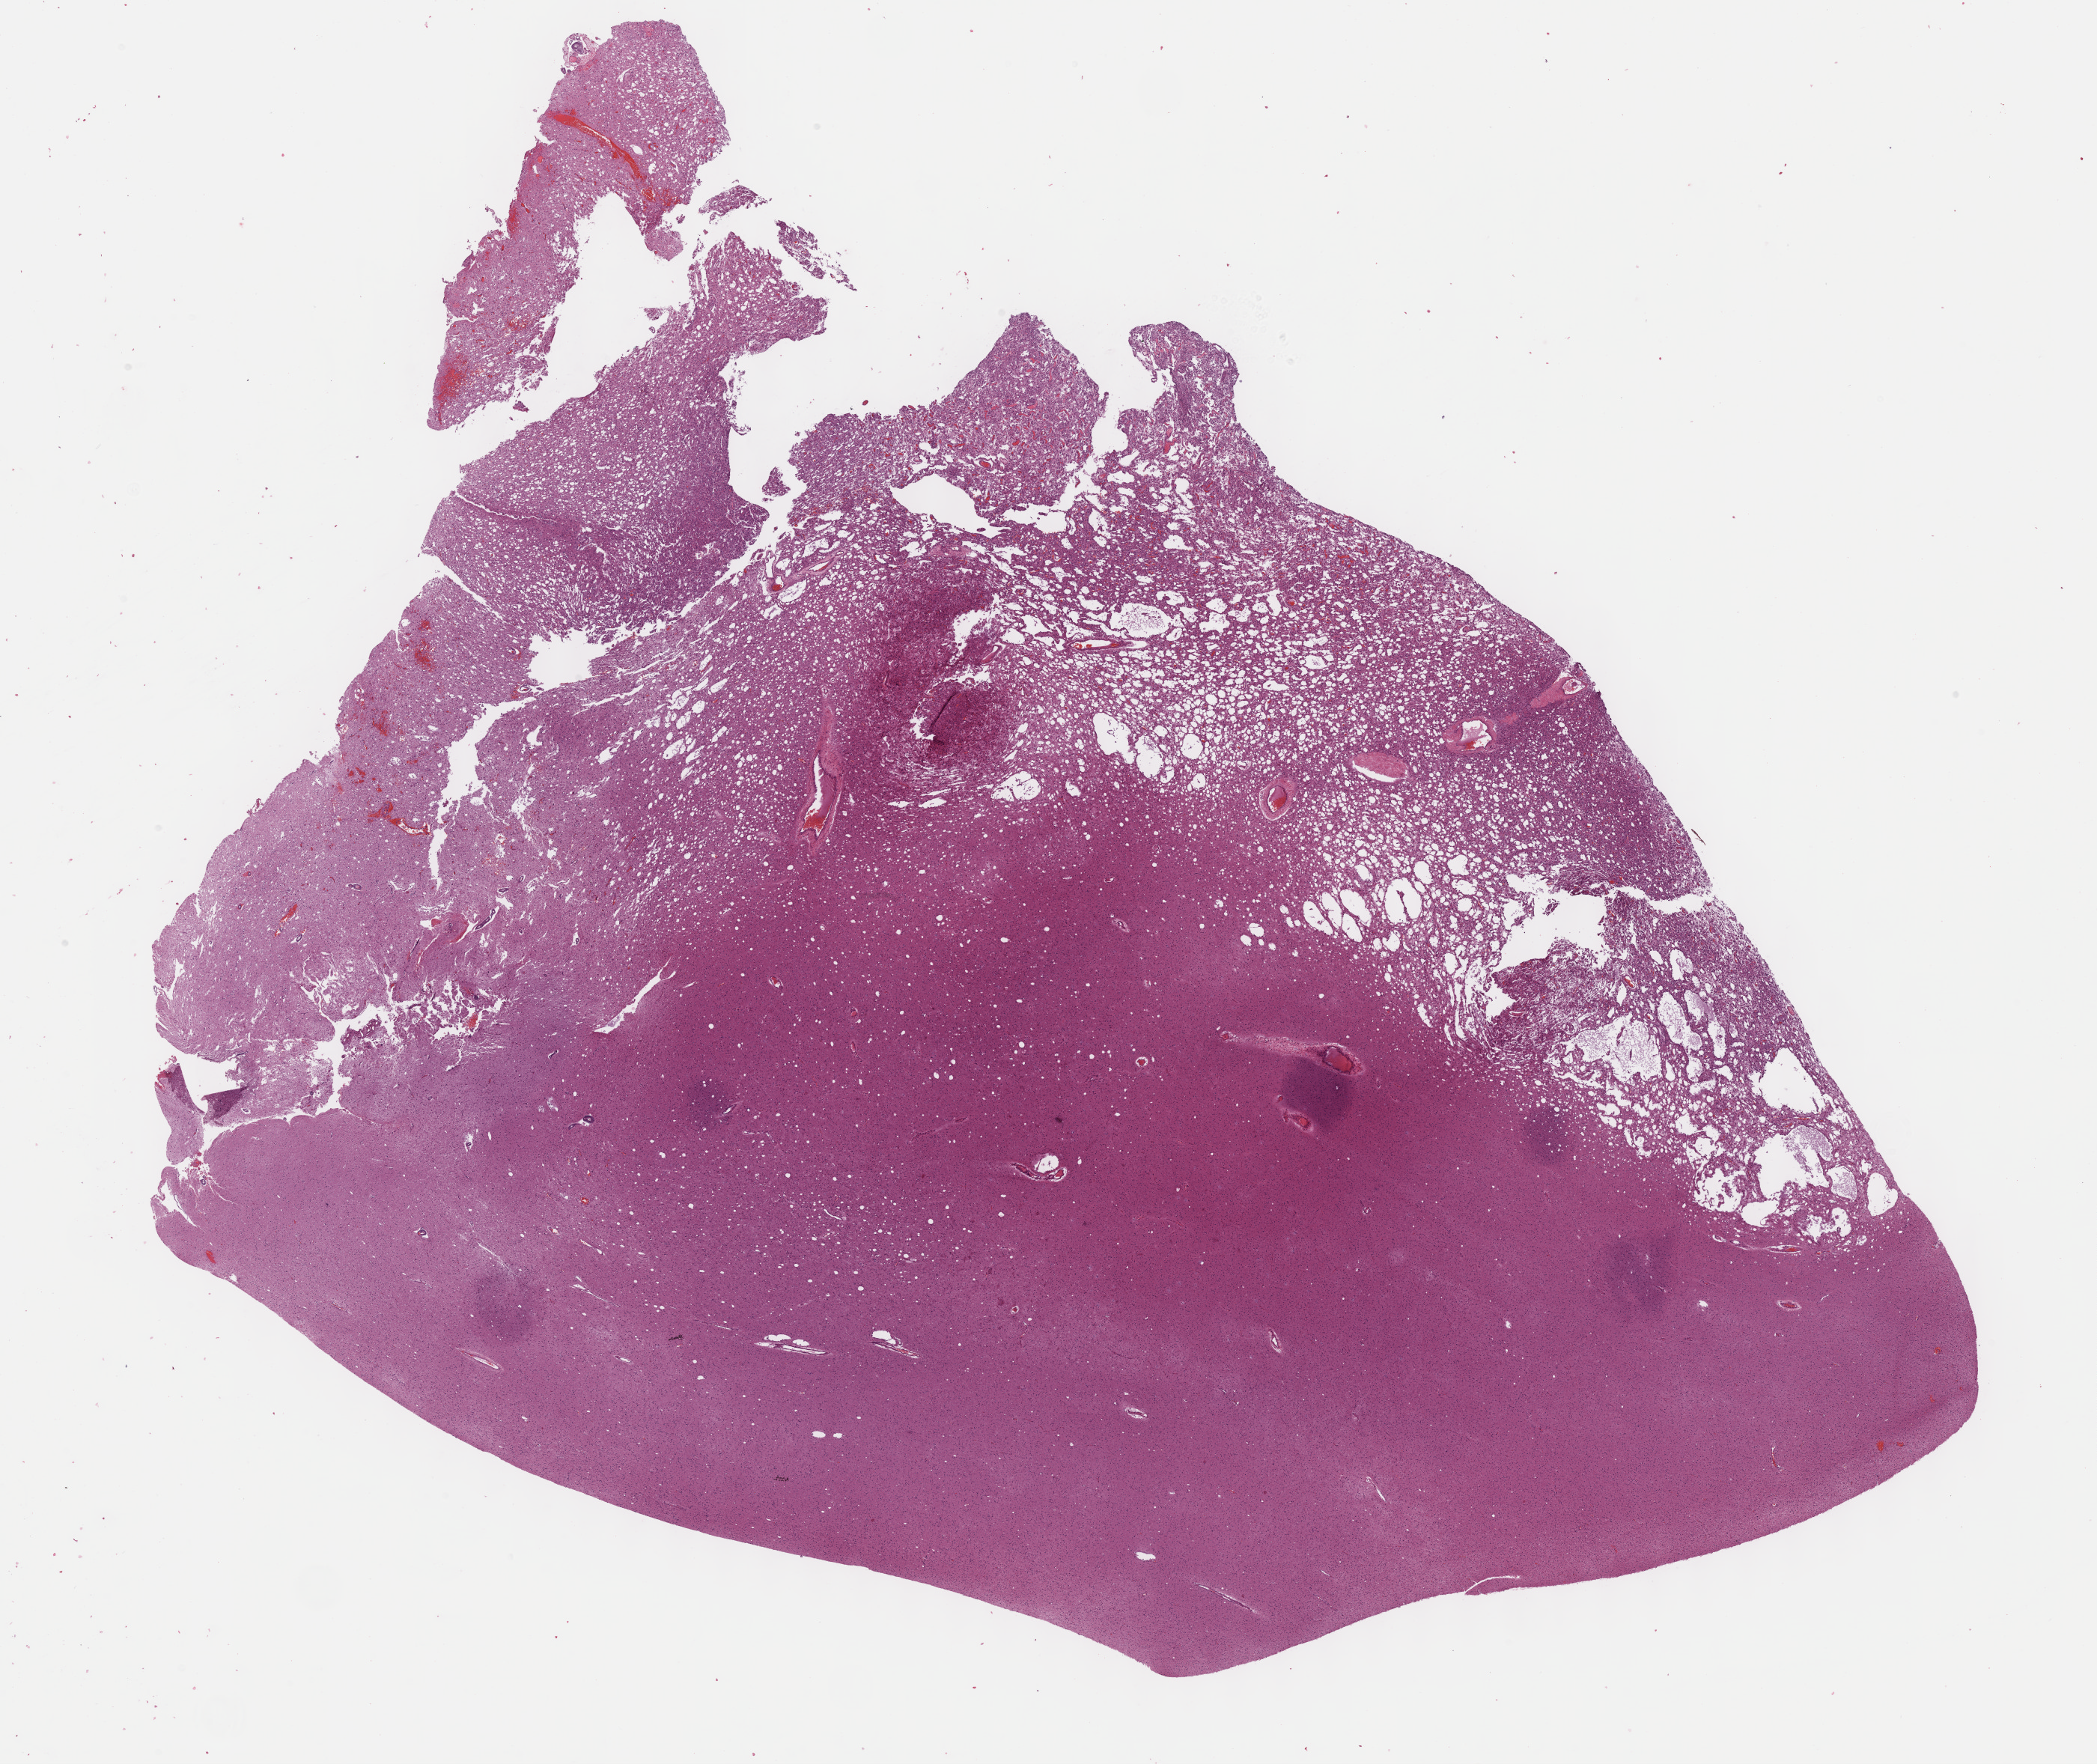
Whole-slide histology image, H&E, whole scanned area (about 22.7 x 19.1 mm, from a 40x scan) shown as a low-resolution overview, formalin-fixed paraffin-embedded (FFPE) diagnostic section, sample: primary tumour, brain. Male, age 61 years at initial diagnosis. Histologic grade: G2 (moderately differentiated).
• laterality: right
• pathologic diagnosis: Mixed glioma (cerebrum)